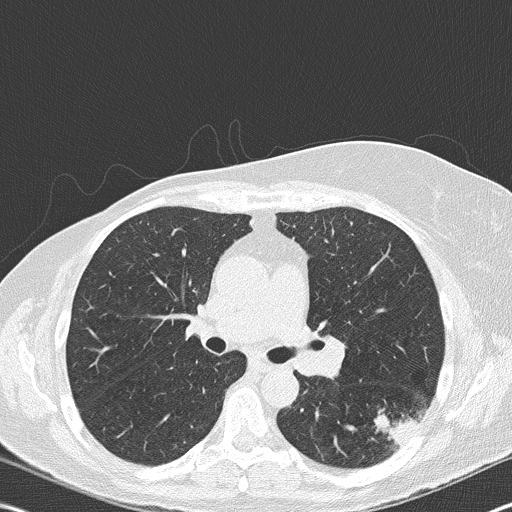
Chest CT (low-dose screening protocol), one axial image. Second annual screen. Lung window (W 1500 / L -600 HU). 2 mm slice thickness. Lung (sharp) reconstruction kernel (B50f). Slice 109 of 177 in the series. 512 × 512 image matrix. Female, age 60 years at enrolment. Current smoker at enrolment.
• Expert-annotated lung lesion, bounding box (x1, y1, x2, y2) in pixels: (368, 386, 435, 450).
• The exam's reader record, not a measurement of the box and not confirmed to be the same lesion: non-calcified nodule or mass ≥4 mm, left lower lobe, 18 × 16 mm, spiculated (stellate) margins, soft tissue attenuation, pre-existing on the prior screen: no.
• Participant outcome: lung cancer diagnosed 35 days after this screen — carcinoma, NOS, left hilum, stage IV (AJCC 6th edition), 45 mm at pathology.